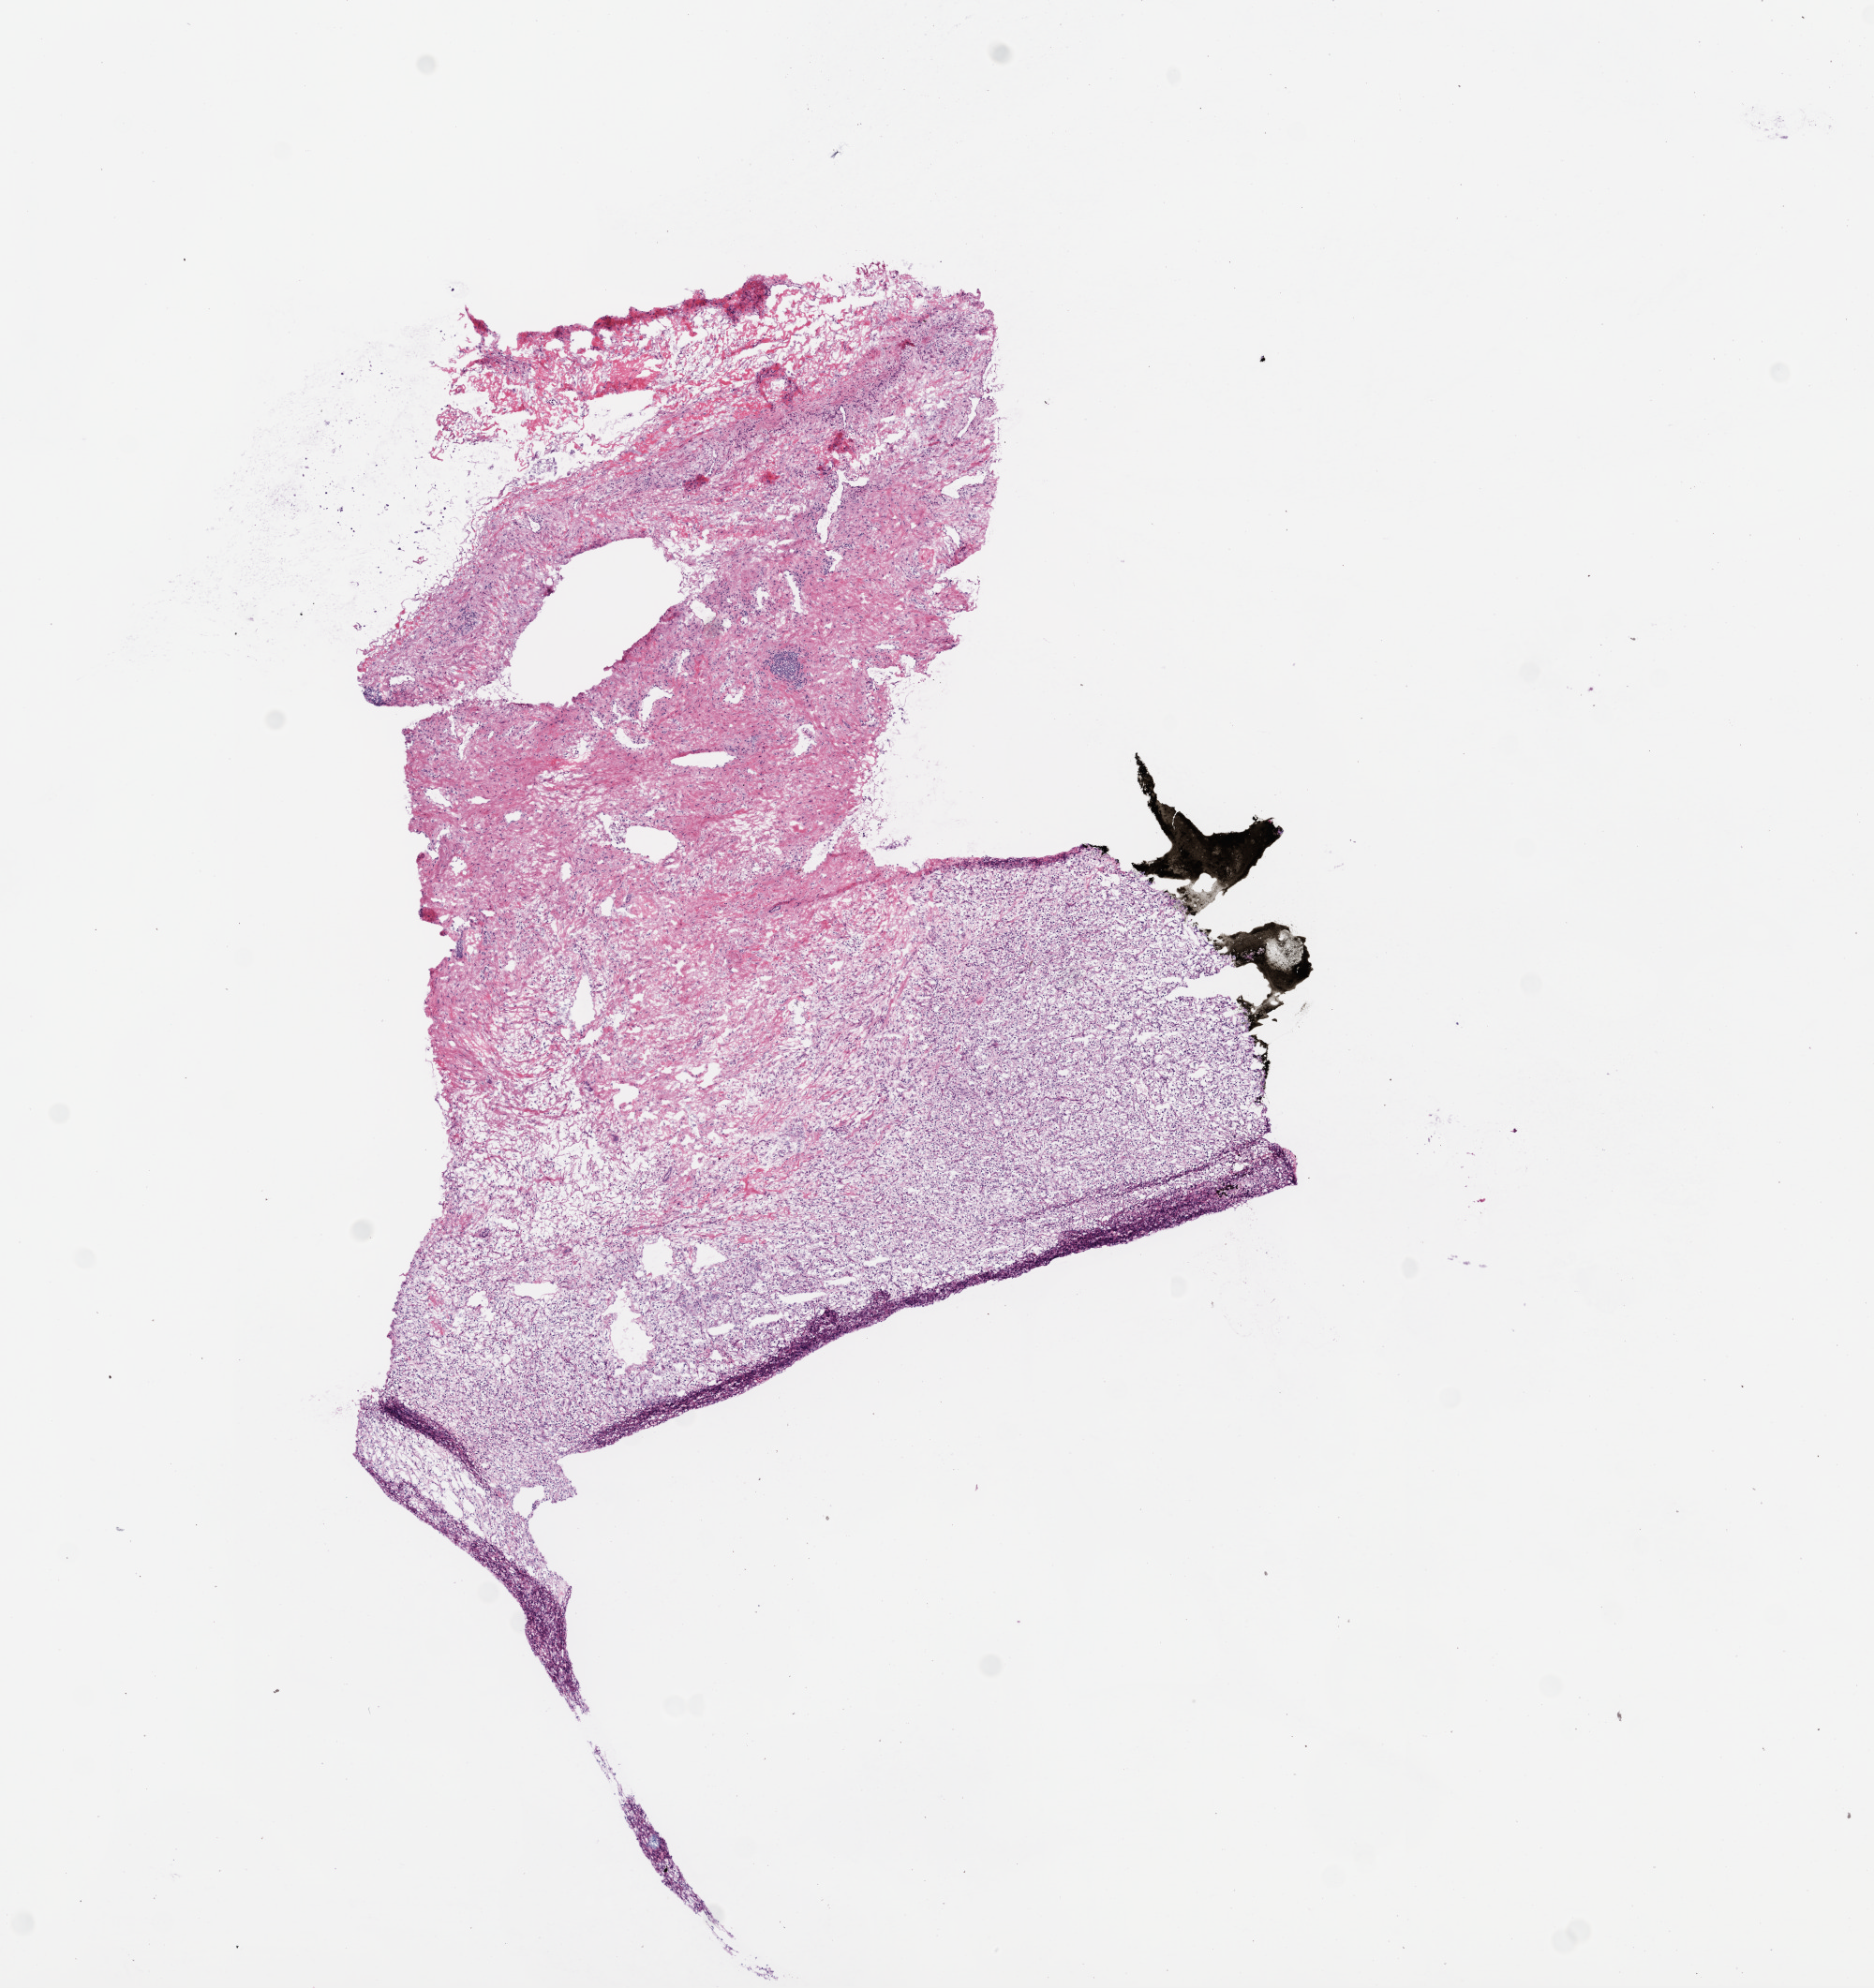
Digitized Hematoxylin and eosin (H&E) stained tissue section (whole slide) — a low-resolution overview of the entire scanned area, about 8.0 x 8.5 mm (slide scanned at 20x); frozen section; primary tumour sample from the kidney. Patient: male, age at initial diagnosis 49 years.
Histologic diagnosis: Clear cell adenocarcinoma, NOS.